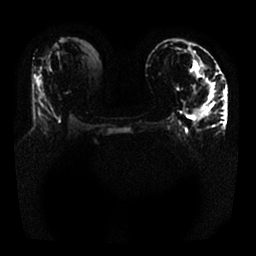
Breast MRI, one axial slice; slice 11 of 25 in the series (ordered by position); diffusion-weighted series; image 2 of 4 stored at this slice position (different b-values; order by instance number); 1.5 T; 4 mm slice thickness; 256 × 256 image matrix, field of view 340 × 340 mm. Female patient.
Annotated regions visible in this slice (expert manual segmentation):
- tumour on diffusion-weighted imaging: bounding box (x1, y1, x2, y2) in pixels: (194, 84, 215, 124)